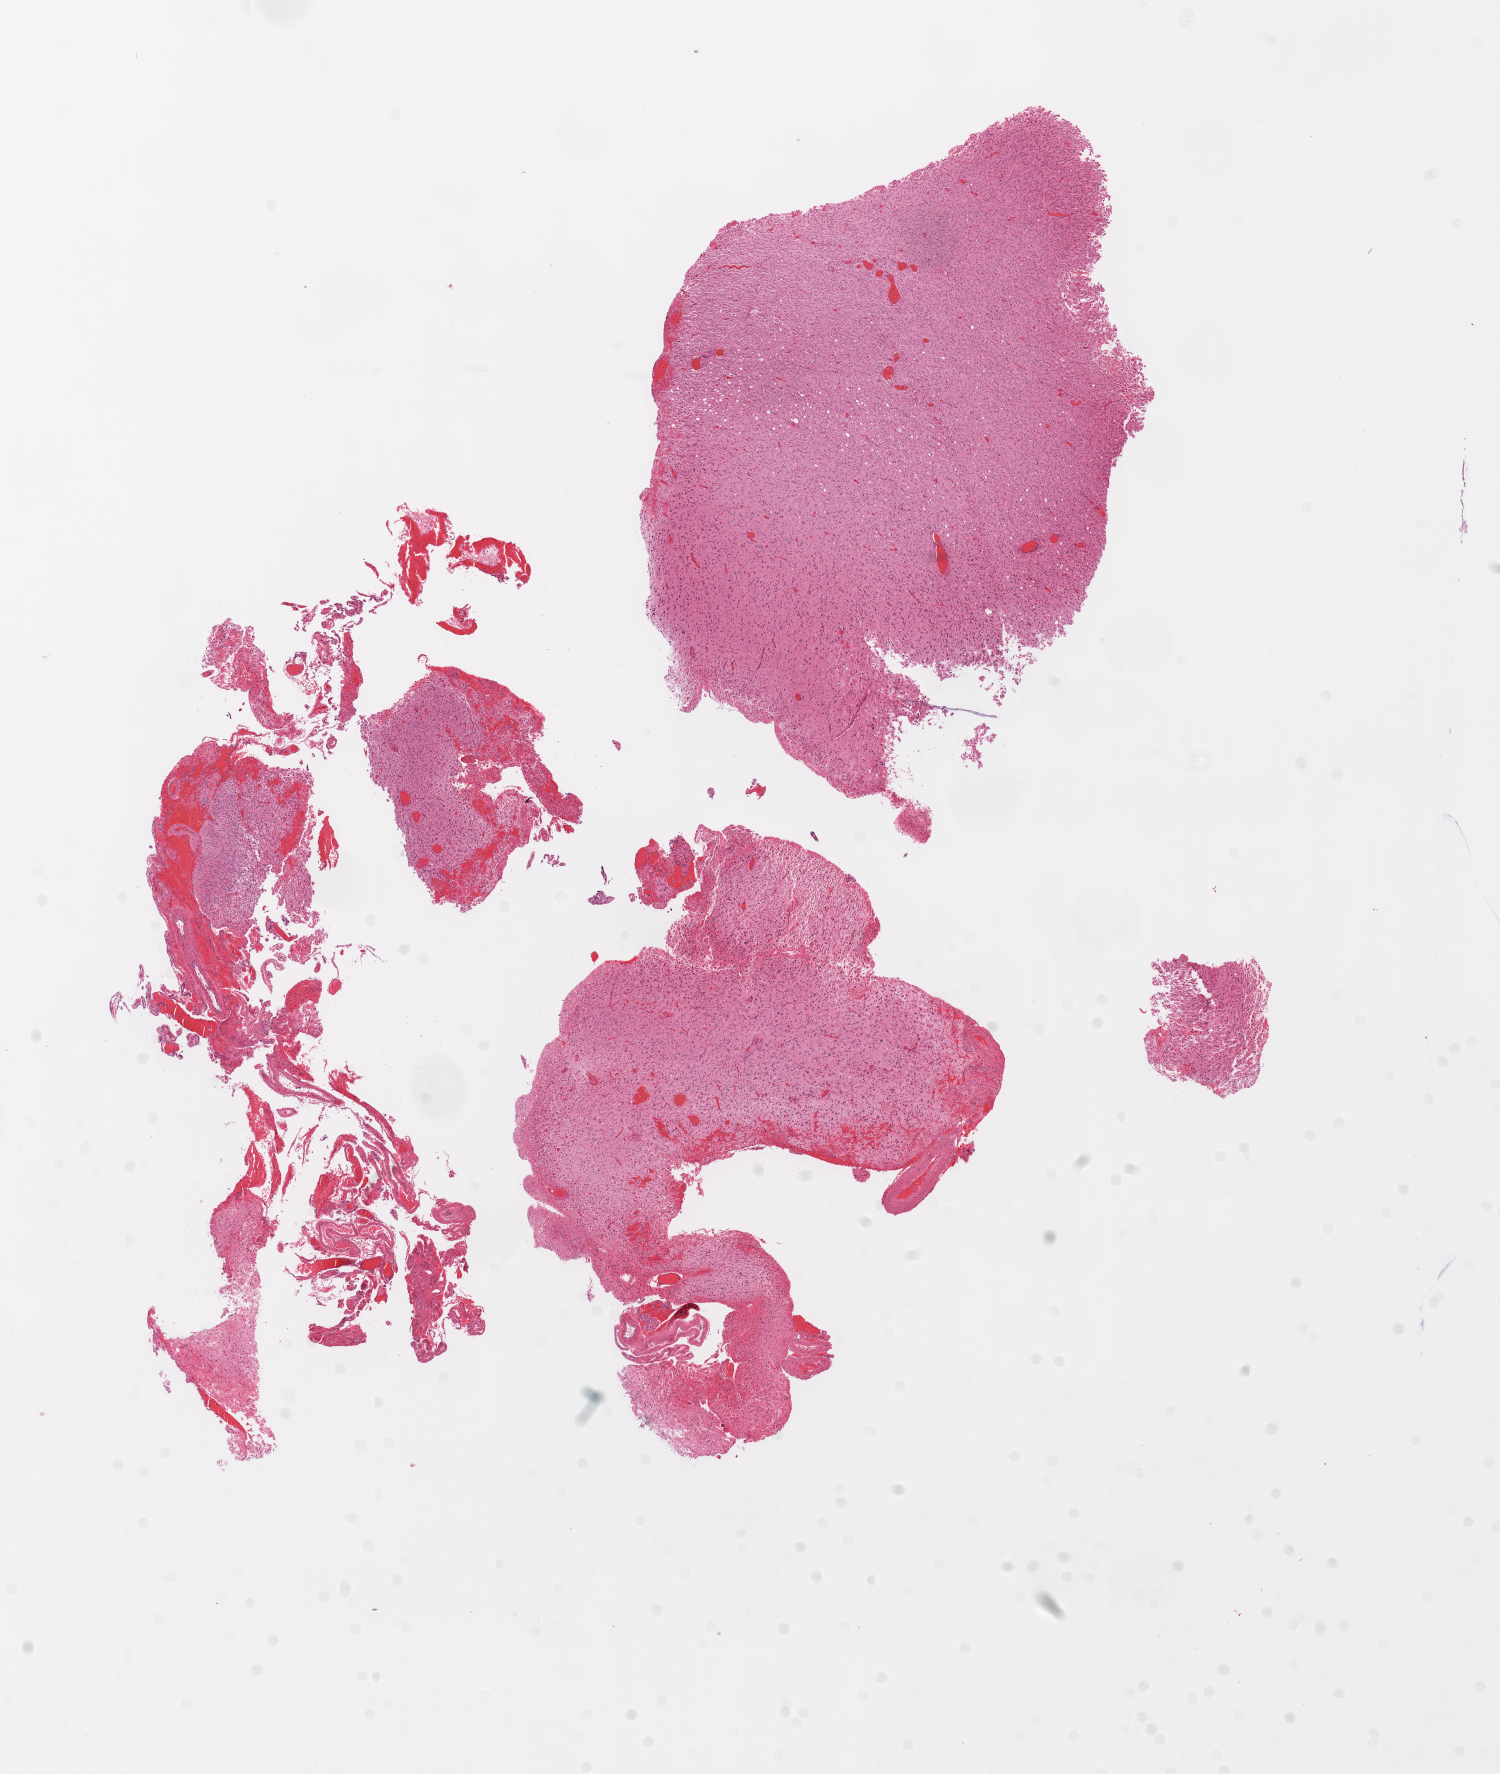
H&E whole-slide image — shown as a low-resolution overview of the whole scanned area (about 12.0 x 14.2 mm). Formalin-fixed paraffin-embedded (FFPE) diagnostic section. Sample: primary tumour, brain. Patient: male, age at initial diagnosis 50 years.
Histologic diagnosis: Glioblastoma.